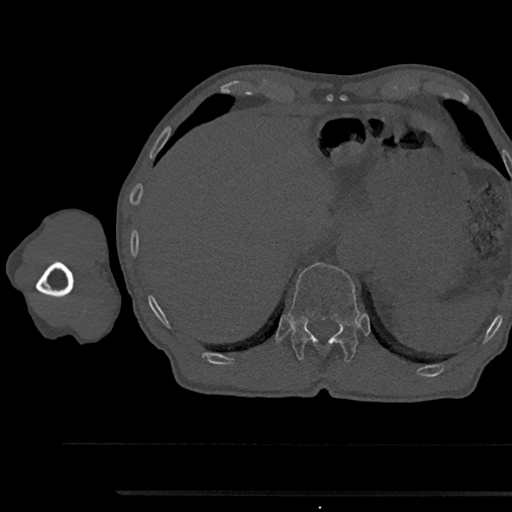
CT including the spine, one axial slice; position 731 of 797 along the scan axis; bone window (W 1800 / L 400 HU); 512 × 512 image matrix, field of view 367 × 367 mm. Male patient, age 79 years. From the clinical record (not read from this slice): primary cancer: prostate.
Outlined on this slice (semi-automatic segmentation, software-assisted and operator-edited):
- T12 vertebra: bounding box <288,262,359,362> (left, top, right, bottom; pixels)